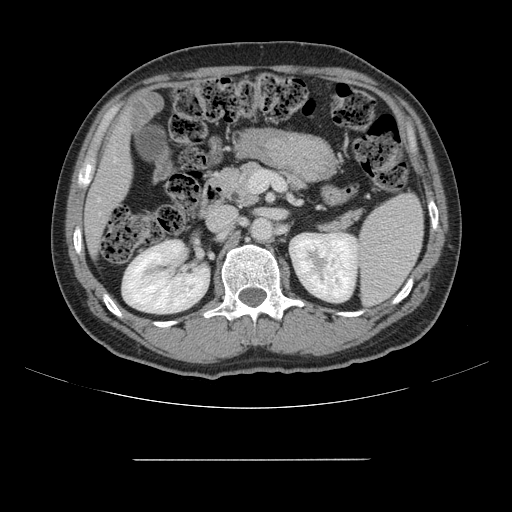
Contrast-enhanced abdominal CT, one axial slice; slice 68 of 164 in the series (ordered by position); 120 kVp; intravenous contrast given; soft-tissue window (W 400 / L 40 HU); 2.5 mm slice thickness; 512 × 512 image matrix. Male patient, age 54 years. Case-level facts recorded for this patient, not image findings: diagnosis: colorectal cancer liver metastases, imaged before liver resection; multiple liver metastases: yes; largest metastasis: 1 cm; disease in both lobes: no.
Annotated regions visible in this slice (outlined manually by an expert reader):
- hepatic veins: box from (x=98, y=198) to (x=101, y=201) px
- liver: (x=85, y=119)–(x=131, y=251)
- planned liver remnant (the part of the liver to remain after resection): (x=85, y=118)–(x=131, y=253)